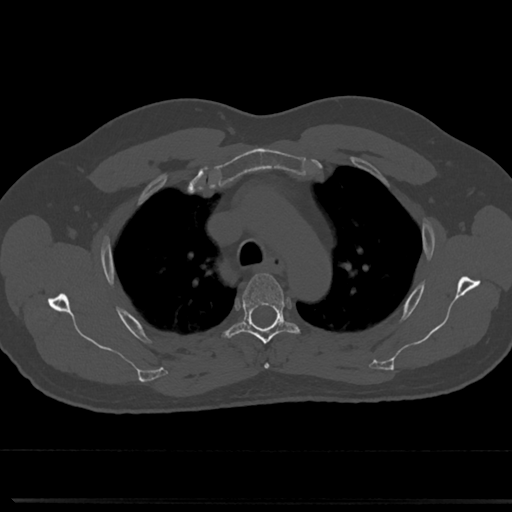
CT including the spine, one axial slice. Position 551 of 817 along the scan axis. Bone window (W 1800 / L 400 HU). 512 × 512 image matrix. Patient: male, 61 years. Case-level facts recorded for this patient, not image findings: primary cancer: prostate.
Structures marked on this image (semi-automatically segmented with operator editing):
- T3 vertebra: box from (x=264, y=363) to (x=269, y=368) px
- T4 vertebra: (x=220, y=273)–(x=301, y=344)